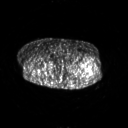
FDG PET of an extremity soft-tissue mass (from a PET/CT study), one axial slice; position 258 of 267 along the scan axis; 128 × 128 image matrix. Patient: female, 62 years. Case-level facts recorded for this patient, not image findings: histological type: undifferentiated – high grade; grade: high; site of the primary tumour: left thigh.
Annotated regions visible in this slice (expert contour drawn on MRI and transferred to this co-registered scan by the dataset authors):
- gross tumour volume including surrounding oedema: bounding box [x1, y1, x2, y2] px = [87, 69, 93, 77]